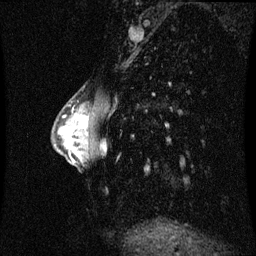
Breast MRI (dynamic contrast-enhanced), one sagittal slice. Dynamic contrast-enhanced series, image 2 of 3 at this slice position (ordered by acquisition). 1.5 T. TE 4.2 ms, TR 8.9 ms. 256 × 256 image matrix, field of view 210 × 210 mm. Patient: female, 33 years. Case-level facts recorded for this patient, not image findings: setting: breast cancer imaged before/during neoadjuvant chemotherapy; receptor status: HER2-positive.
Outlined on this slice (semi-automatic segmentation, software-assisted and operator-edited):
- analysis volume of interest (the breast-tissue region the enhancement analysis was run in; not a lesion): bounding box <66,106,93,141> (left, top, right, bottom; pixels)
- tumour enhancement mask (voxels above the 70 % enhancement threshold inside the analysis volume of interest): <82,117,86,127>